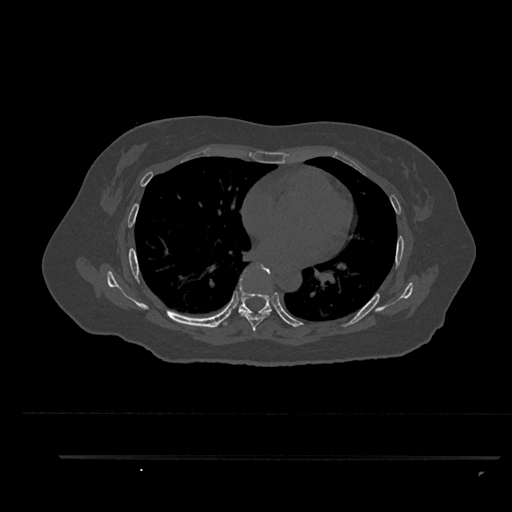
CT including the spine, one axial slice. Slice 534 of 797 in the series (ordered by position). 120 kVp. Bone window (W 1800 / L 400 HU). 0.5 mm slice thickness. 512 × 512 image matrix. Patient: female, 44 years. Case-level facts recorded for this patient, not image findings: primary cancer: renal; vertebrae with lytic lesions (as recorded): L1.
Annotated regions visible in this slice (semi-automatic segmentation, software-assisted and operator-edited):
- T6 vertebra: box from (x=240, y=312) to (x=271, y=333) px
- T7 vertebra: (x=224, y=270)–(x=272, y=326)